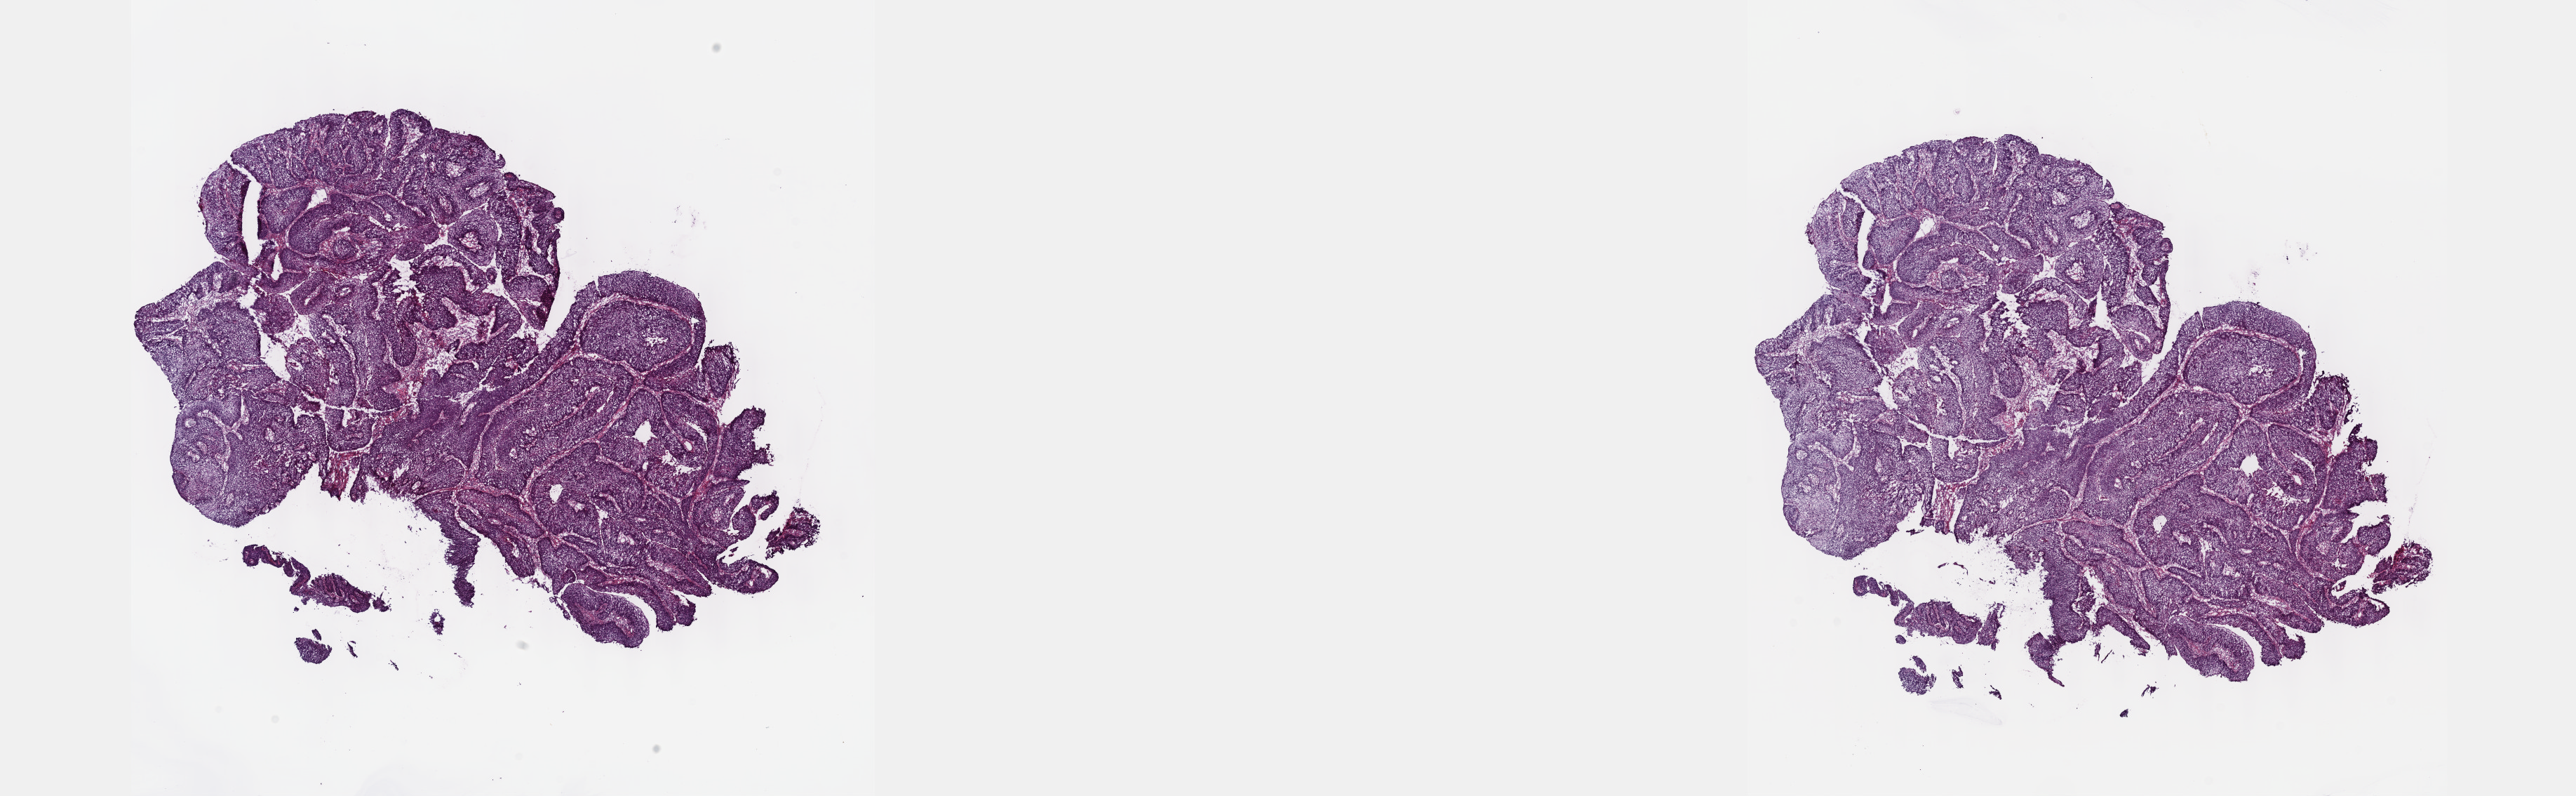
Digitized Hematoxylin and eosin (H&E) stained tissue section (whole slide) — shown as a low-resolution overview of the whole scanned area (about 29.7 x 9.2 mm, acquisition: 40x scan); frozen section from the top of the tissue portion; primary tumour sample from the esophagus. Patient: male, age at initial diagnosis 49 years. Histologic grade: G1 (well differentiated). Pathologist review of this section (percent, as recorded): tumour cells 80%, tumour nuclei 80%, normal cells 0%, stromal cells 15%, necrosis 5%. Inflammatory infiltration, as recorded: lymphocyte infiltration 40%, monocyte infiltration 20%, neutrophil infiltration 20%.
Pathologic diagnosis: Squamous cell carcinoma, NOS. Lymph nodes positive (case pathology): 1 of 10 examined. AJCC pathologic stage: IIB (7th edition).